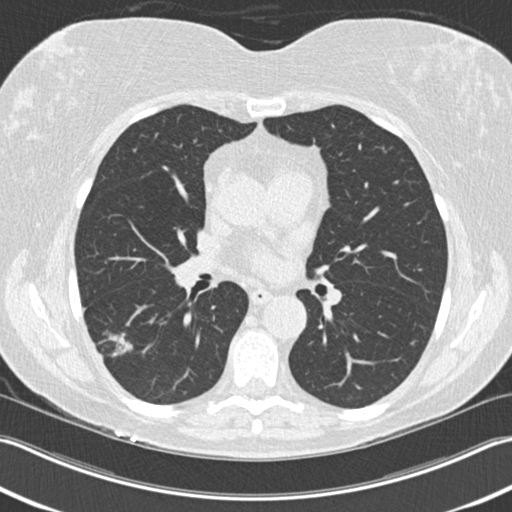
Axial slice from a low-dose chest CT screening exam; baseline annual screen; lung window (W 1500 / L -600 HU); 2 mm slice thickness; 512 × 512 image matrix, field of view 348 × 348 mm. Female participant, aged 63 years at enrolment.
Expert-annotated lung lesion, box from (x=87, y=321) to (x=146, y=373) px. The screening reader recorded 3 non-calcified nodules or masses ≥4 mm on this exam; which of them this box marks is not recorded. Lung cancer was diagnosed 57 days after this screen: bronchiolo-alveolar adenocarcinoma, NOS, right lower lobe, well differentiated (G1), stage IA (AJCC 6th edition), 25 mm at pathology.